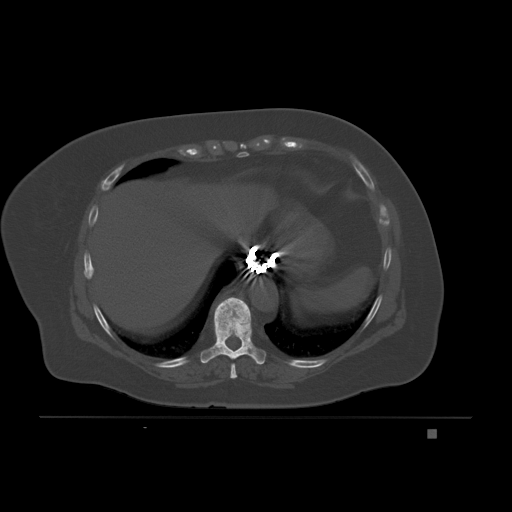
CT including the spine, one axial slice; position 110 of 221 along the scan axis; bone window (W 1800 / L 400 HU); 3 mm slice thickness; 512 × 512 image matrix, field of view 474 × 474 mm. Patient: female, 63 years. From the clinical record (not read from this slice): primary cancer: breast.
Annotated regions visible in this slice (semi-automatically segmented with operator editing):
- T8 vertebra: bounding box <230,363,237,379> (left, top, right, bottom; pixels)
- T9 vertebra: <200,297,267,364>